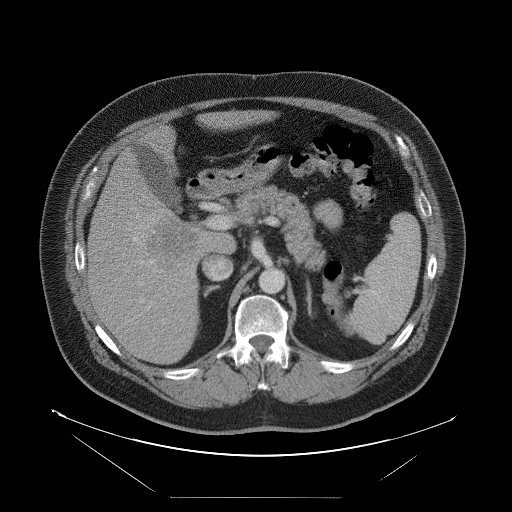
Contrast-enhanced abdominal CT, one axial slice. Position 54 of 114 along the scan axis. Intravenous contrast given. Soft-tissue window (W 400 / L 40 HU). 5 mm slice thickness. 512 × 512 image matrix. Male patient, age 61 years. Case-level facts recorded for this patient, not image findings: diagnosis: colorectal cancer liver metastases, imaged before liver resection; multiple liver metastases: no; largest metastasis: 6.5 cm; disease in both lobes: yes.
Structures marked on this image (manually delineated by an expert):
- hepatic veins: box from (x=134, y=238) to (x=136, y=240) px
- liver: (x=89, y=111)–(x=265, y=365)
- planned liver remnant (the part of the liver to remain after resection): (x=140, y=112)–(x=264, y=172)
- liver metastasis: (x=148, y=220)–(x=198, y=271)